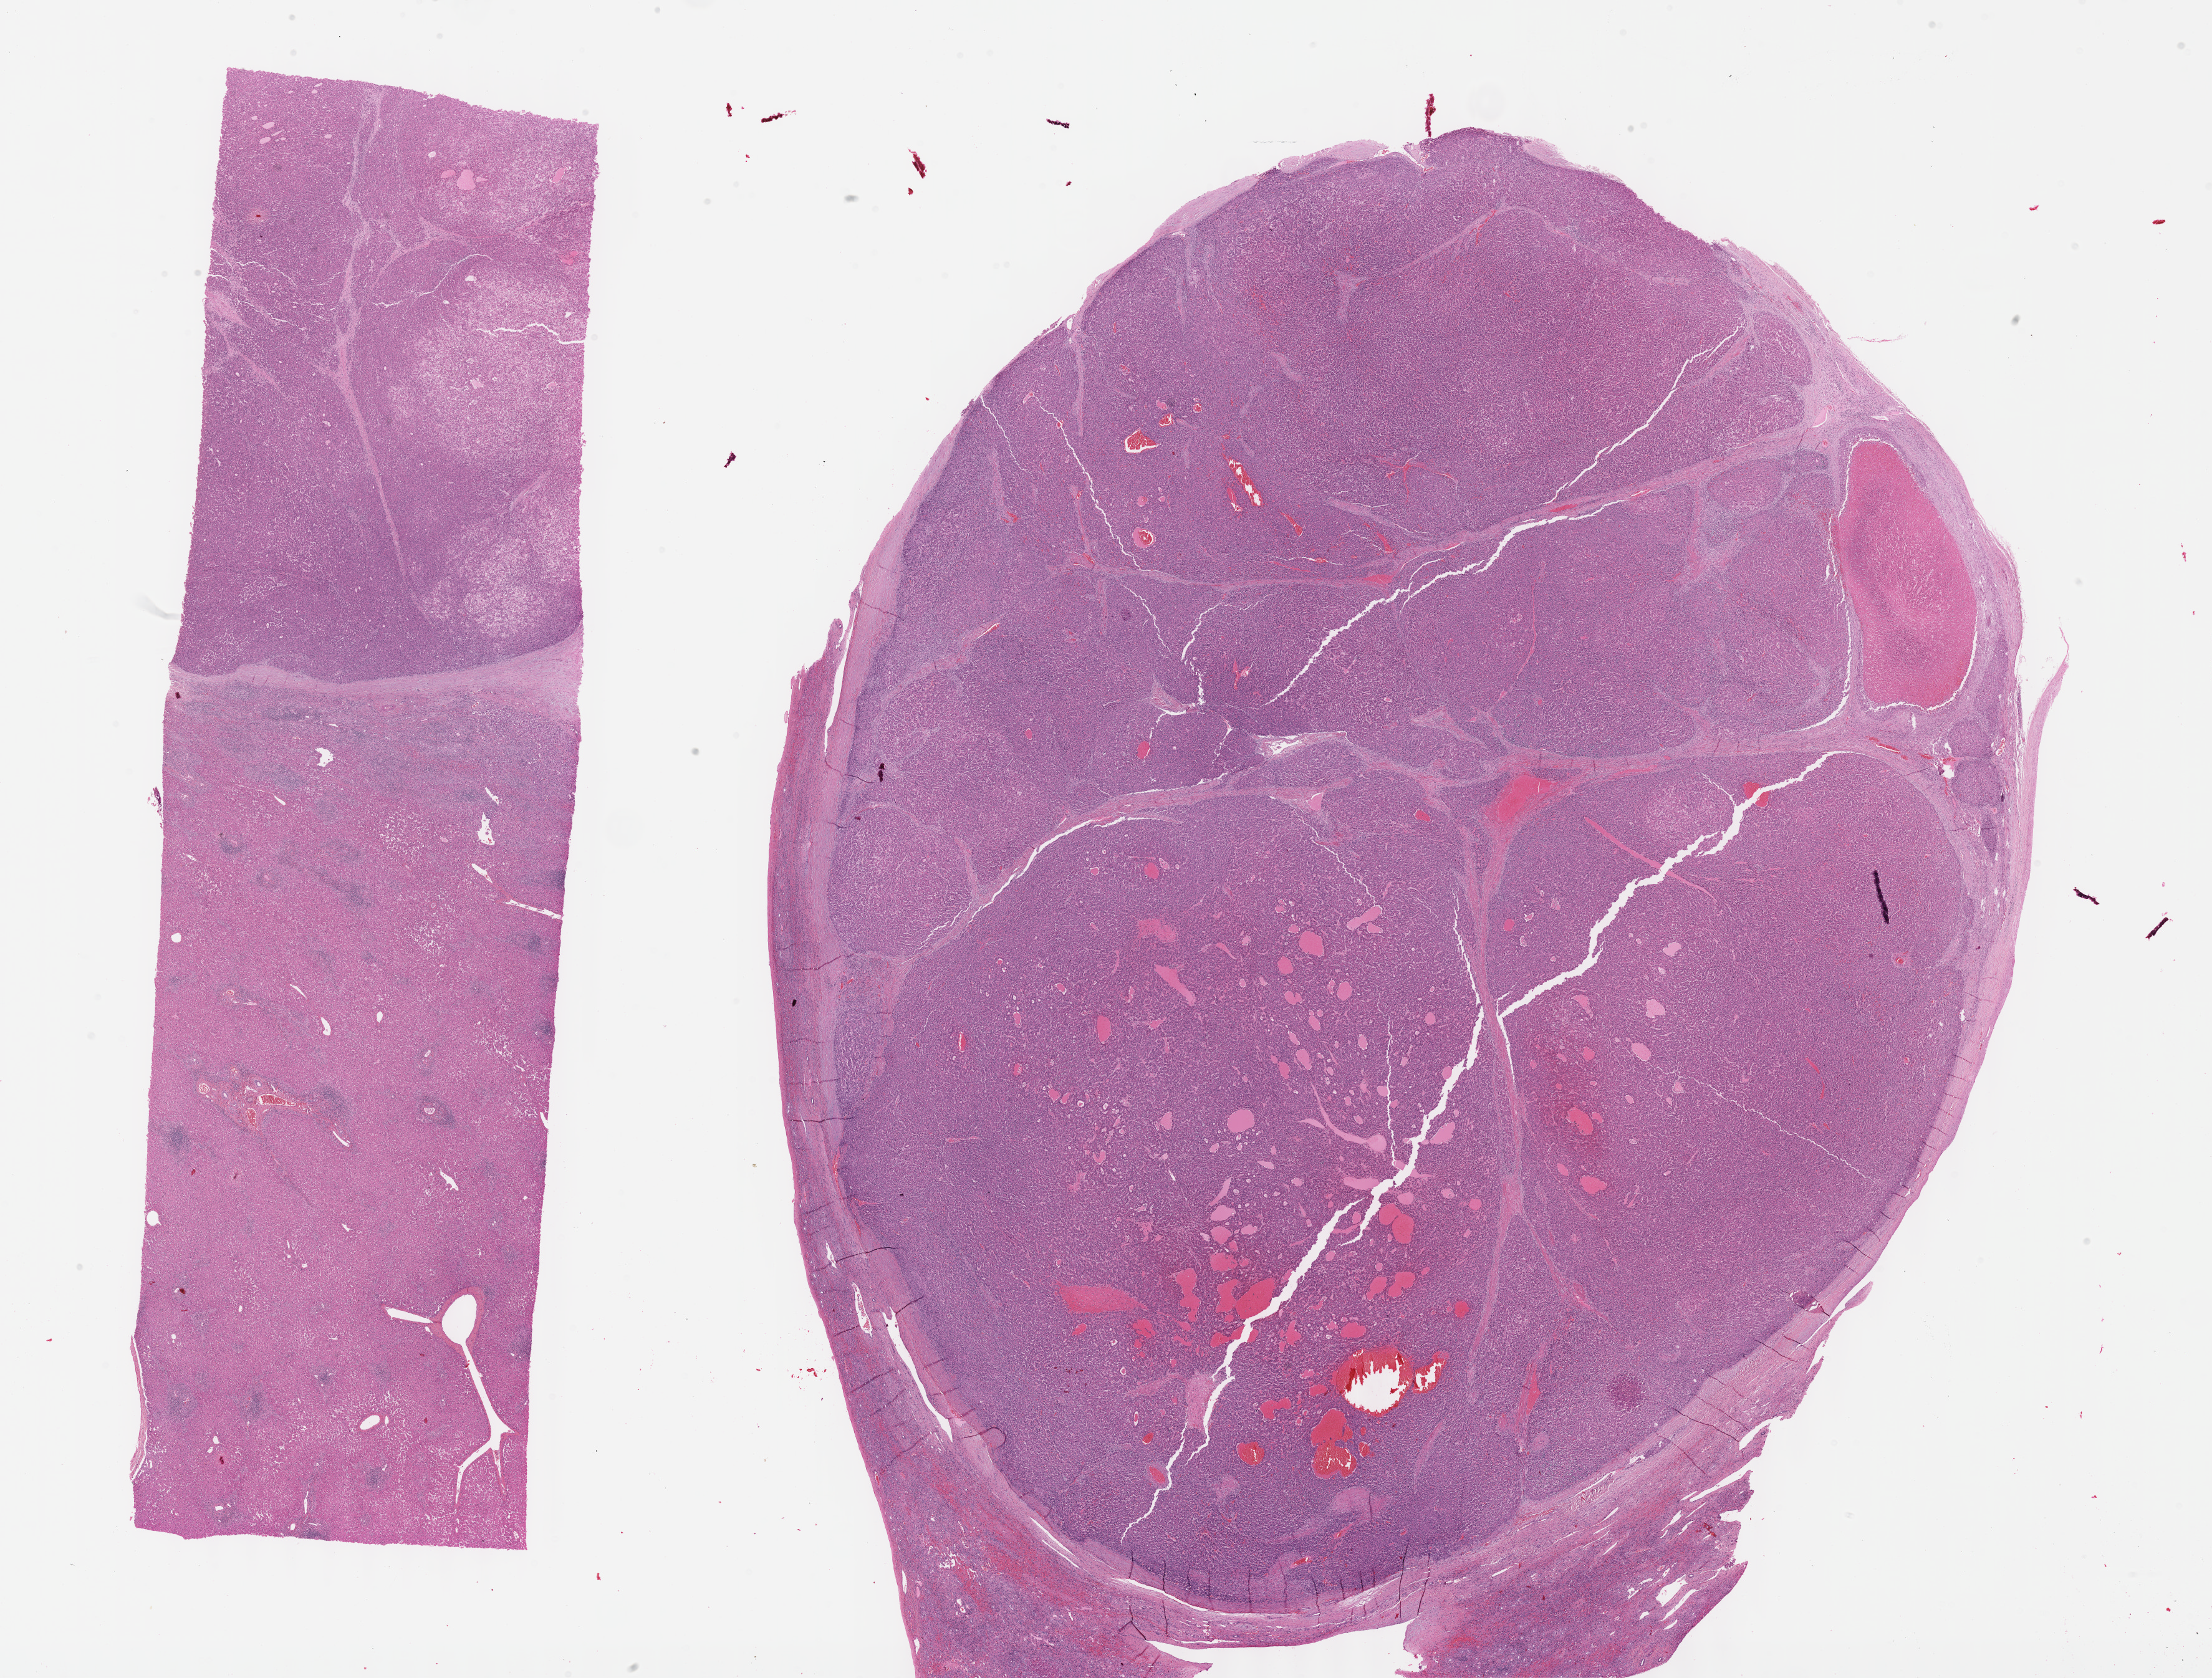
Digitized H&E tissue section (whole slide), a low-resolution overview of the entire scanned area, about 28.7 x 21.8 mm. FFPE section. Liver, primary tumour sample. Male, age 16 years at initial diagnosis.
Histologic diagnosis: Hepatocellular carcinoma, NOS.